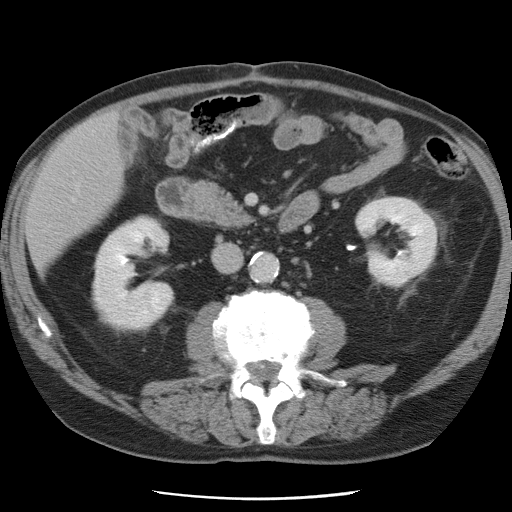
Contrast-enhanced abdominal CT, one axial slice; position 23 of 78 along the scan axis; soft-tissue window (W 400 / L 40 HU); 5 mm slice thickness; 512 × 512 image matrix, field of view 337 × 337 mm. Male patient, age 75 years. From the clinical record (not read from this slice): diagnosis: colorectal cancer liver metastases, imaged before liver resection; multiple liver metastases: yes; largest metastasis: 2.4 cm; disease in both lobes: yes.
Structures marked on this image (expert manual segmentation):
- liver: bounding box <27,115,121,270> (left, top, right, bottom; pixels)
- planned liver remnant (the part of the liver to remain after resection): <27,120,122,269>